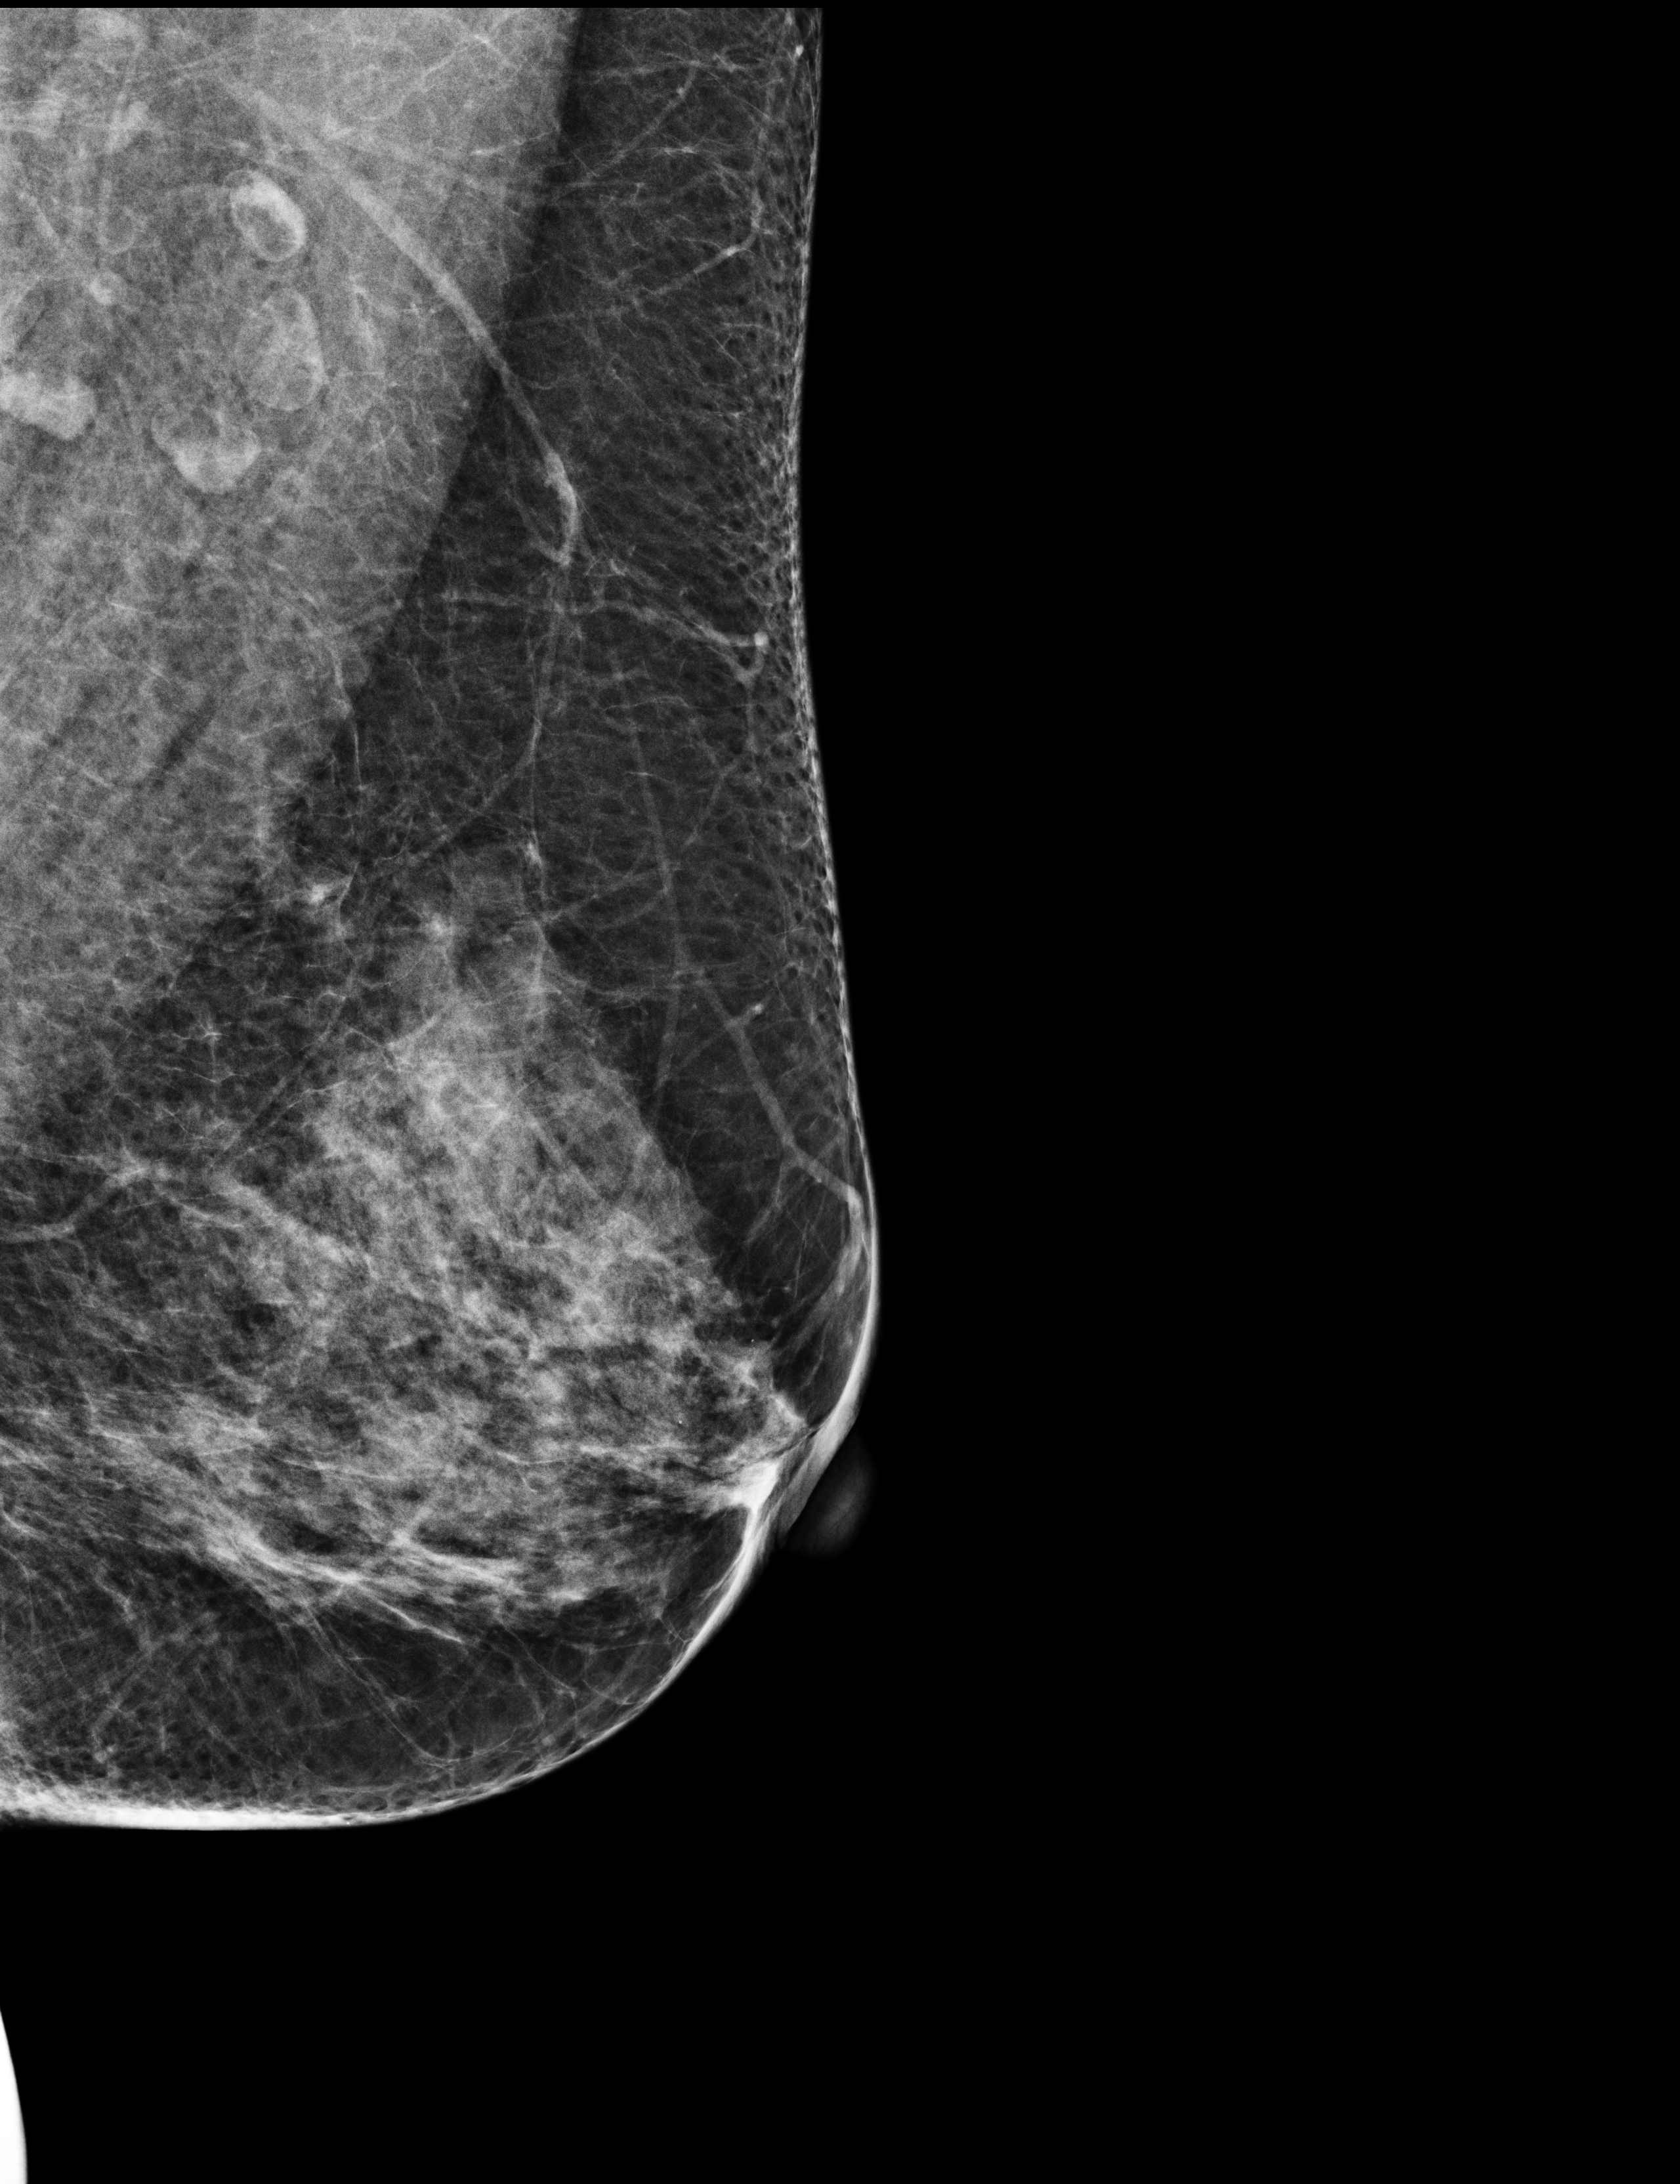
Annual screening mammography examination; compressed breast thickness 53 mm. Patient: female, 58 years.
Image type: full-field digital mammogram. Breast: left. Projection: medio-lateral oblique projection.